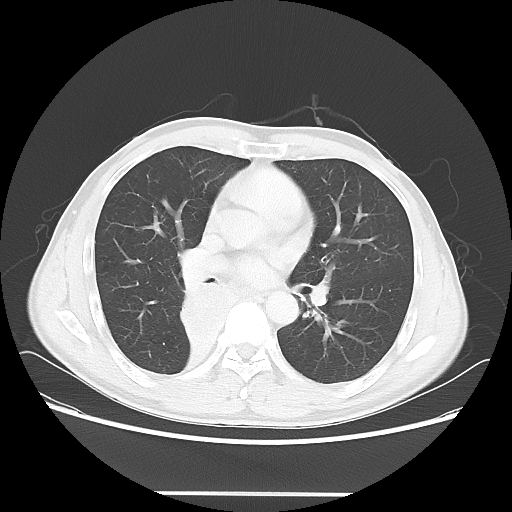
Chest CT, one axial slice. Slice 33 of 62 in the series (ordered by position). Reconstruction kernel LUNG. 120 kVp. Lung window (W 1500 / L -600 HU). 5 mm slice thickness. 512 × 512 image matrix. Male patient, age 47 years. Case-level facts recorded for this patient, not image findings: clinical TNM (as recorded): T2 N0 M0; histopathological grade: G2.
Annotated regions visible in this slice (rectangle marked by the reading radiologist):
- lung tumour (recorded histology: squamous cell carcinoma): bounding box (x1, y1, x2, y2) in pixels: (176, 279, 239, 353)